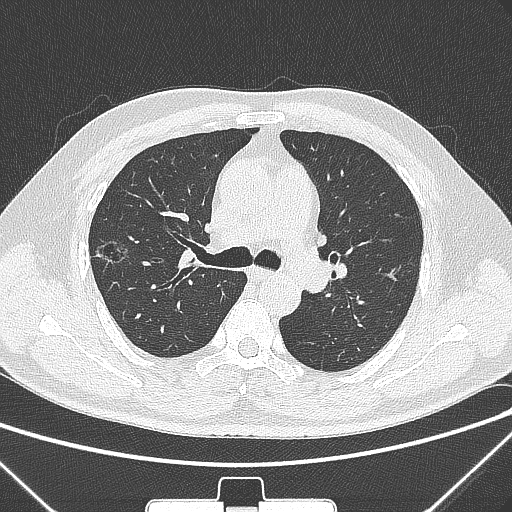
Chest CT, one axial slice. Position 198 of 320 along the scan axis. Lung window (W 1500 / L -600 HU). 1 mm slice thickness. 512 × 512 image matrix, field of view 350 × 350 mm. Patient: male, 58 years. Case-level facts recorded for this patient, not image findings: clinical TNM (as recorded): T1c N0 M0; histopathological grade: G2.
Annotated regions visible in this slice (rectangle marked by the reading radiologist):
- lung tumour (recorded histology: adenocarcinoma): box from (x=90, y=230) to (x=130, y=278) px